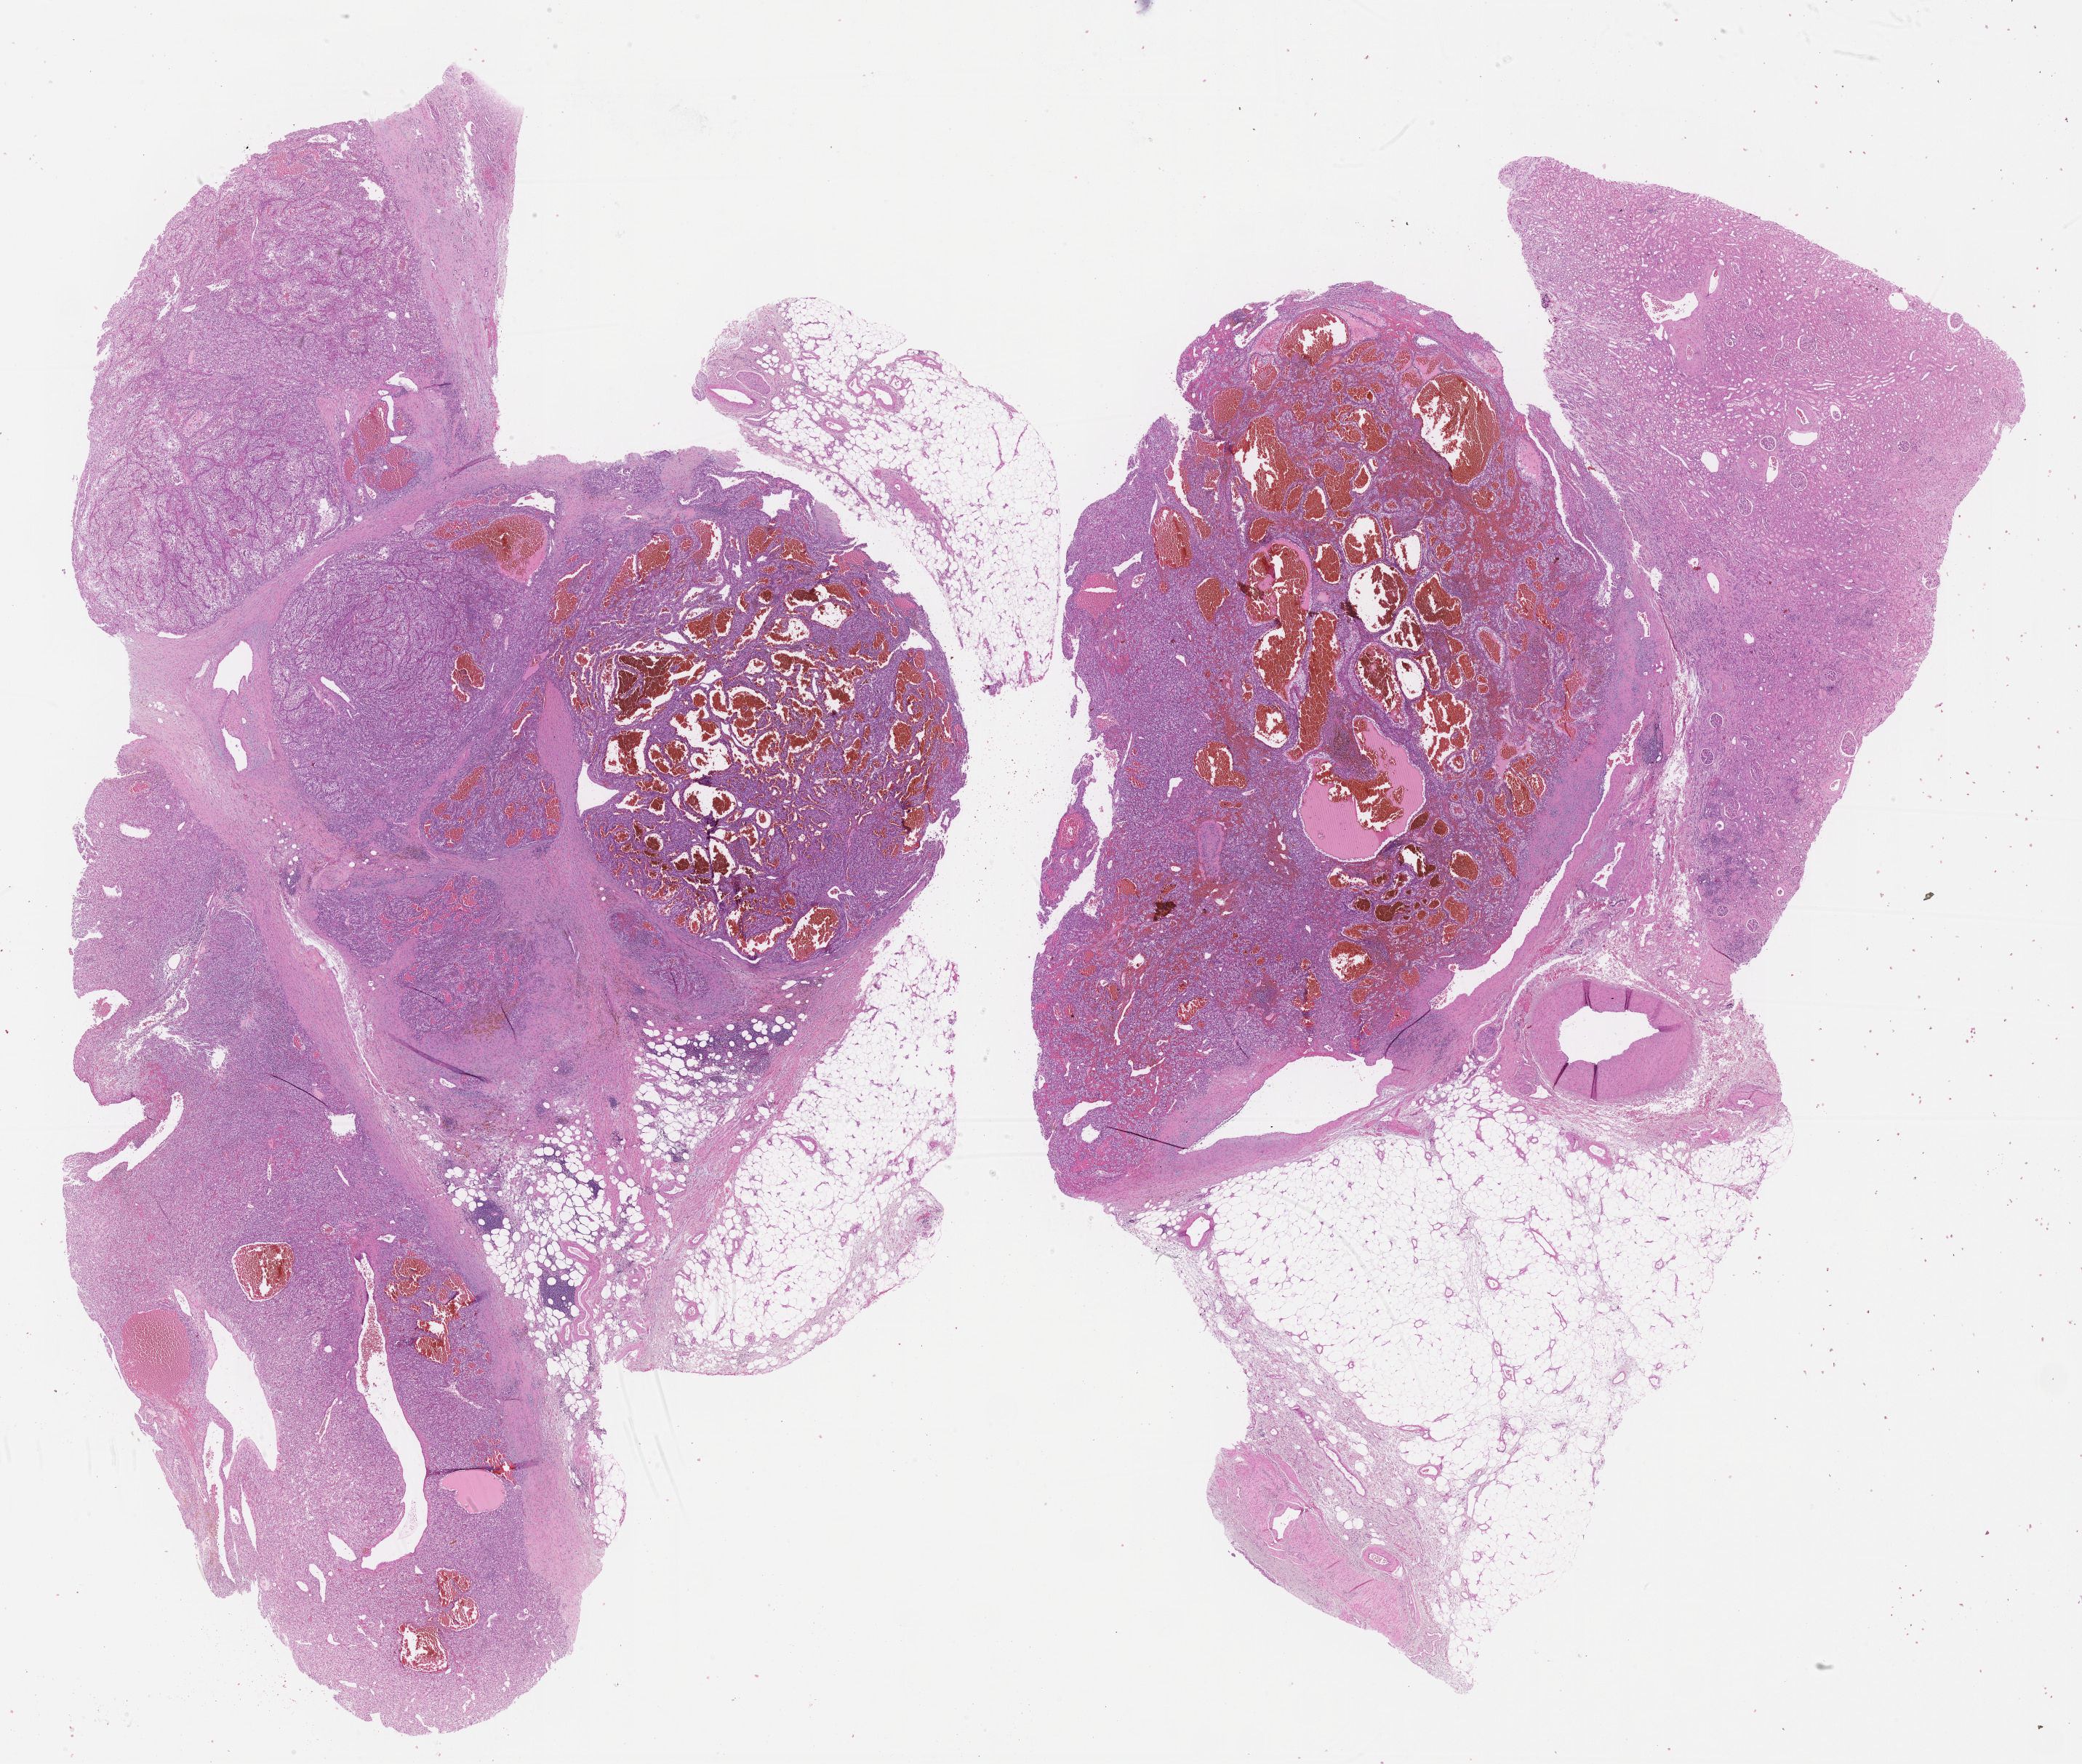
Hematoxylin and eosin (H&E) stained whole-slide image, shown as a low-resolution overview of the whole scanned area (about 23.1 x 19.6 mm, from a 40x scan); FFPE section; primary tumour sample from the kidney. Patient: male, age at initial diagnosis 49 years. Histologic grade: G4 (undifferentiated).
* AJCC pathologic stage: III (7th edition)
* laterality: left
* diagnosis: Clear cell adenocarcinoma, NOS